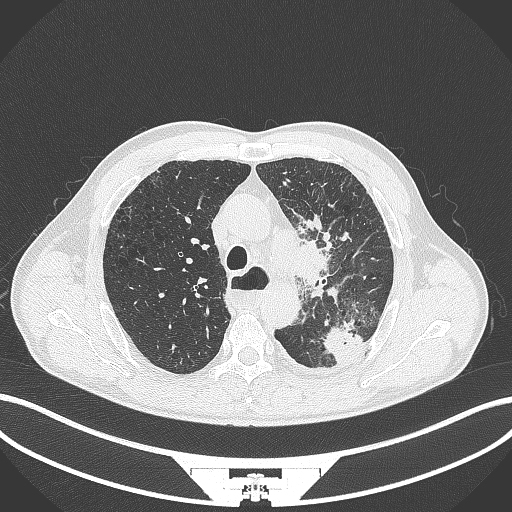
Chest CT, one axial slice. Position 280 of 411 along the scan axis. Lung window (W 1500 / L -600 HU). 1 mm slice thickness. 512 × 512 image matrix, field of view 400 × 400 mm. Male patient, age 57 years. Case-level facts recorded for this patient, not image findings: clinical TNM (as recorded): T2a N1 M0.
Outlined on this slice (rectangle marked by the reading radiologist):
- lung tumour (recorded histology: squamous cell carcinoma): box from (x=292, y=239) to (x=333, y=291) px